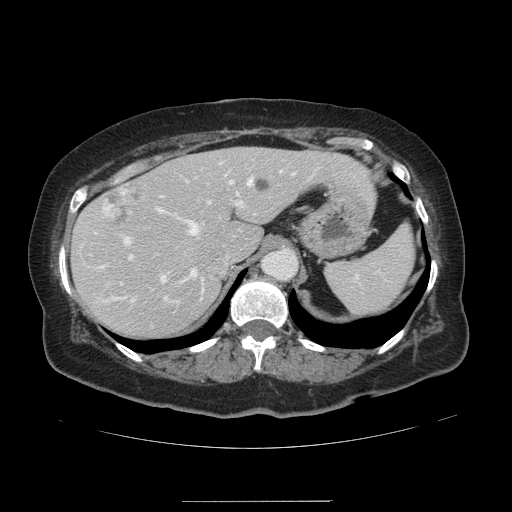
Contrast-enhanced abdominal CT, one axial slice; slice 94 of 141 in the series (ordered by position); intravenous contrast given; soft-tissue window (W 400 / L 40 HU); 2.5 mm slice thickness; 512 × 512 image matrix. Female patient, age 74 years. From the clinical record (not read from this slice): diagnosis: colorectal cancer liver metastases, imaged before liver resection; multiple liver metastases: yes; largest metastasis: 7 cm; disease in both lobes: yes.
Annotated regions visible in this slice (outlined manually by an expert reader):
- hepatic veins: bounding box (x1, y1, x2, y2) in pixels: (155, 179, 252, 283)
- liver: (73, 148, 371, 340)
- planned liver remnant (the part of the liver to remain after resection): (73, 148, 371, 340)
- portal vein (with intrahepatic branches): (120, 162, 294, 301)
- liver metastasis: (257, 180, 270, 192)
- liver metastasis: (102, 186, 141, 230)